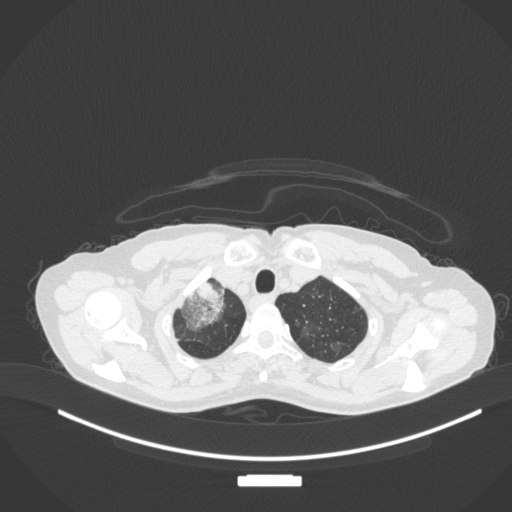
Chest CT, one axial slice; position 291 of 311 along the scan axis; lung window (W 1500 / L -600 HU); 512 × 512 image matrix. Female patient, age 59 years. From the clinical record (not read from this slice): clinical TNM (as recorded): T3 N0 M0; histopathological grade: G1.
Annotated regions visible in this slice (bounding box drawn by a radiologist):
- lung tumour (recorded histology: adenocarcinoma): bounding box (x1, y1, x2, y2) in pixels: (175, 273, 228, 333)